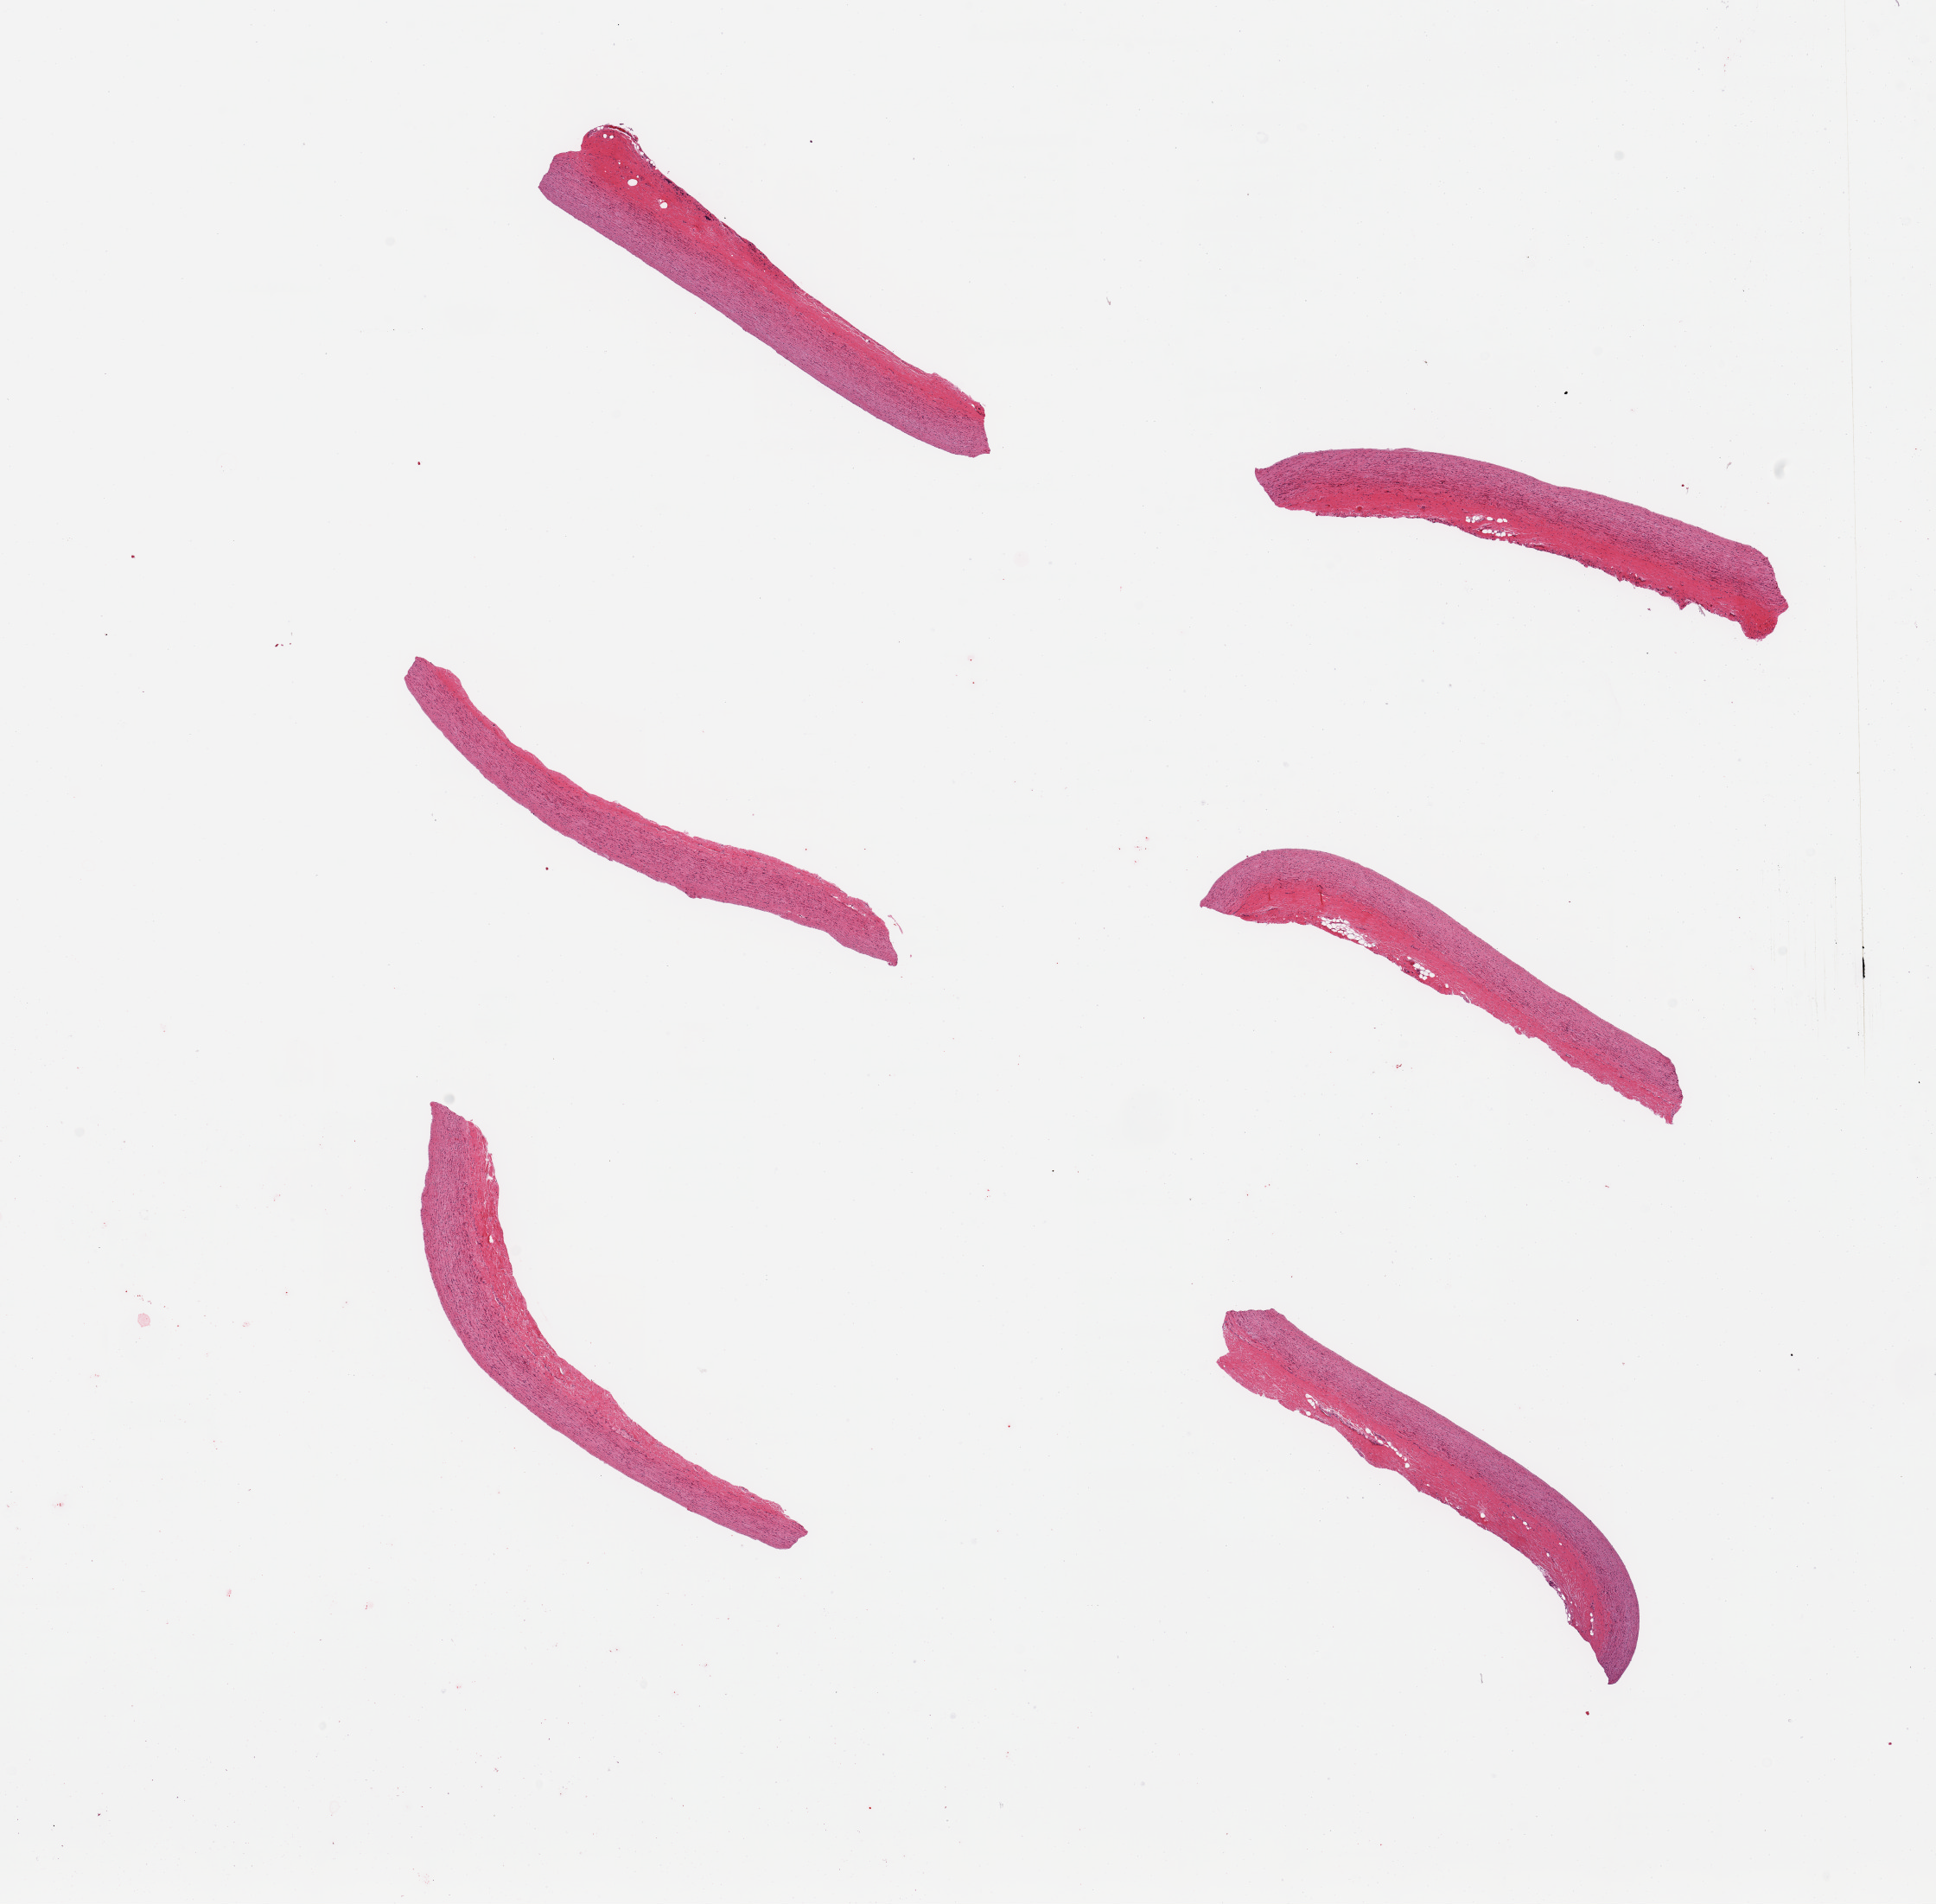
Whole-slide image, H&E stain, shown as a low-resolution overview of the whole scanned area (about 17.7 x 17.4 mm, from a 20x scan); PAXgene-fixed paraffin-embedded (PFPE) section; sampled site (target tissue): aorta; donor tissue sample. Donor sex: female.
Reviewer comment on this tissue sample: 6 pieces; no plaques; well formed mural fibers; well trimmed of external fat.